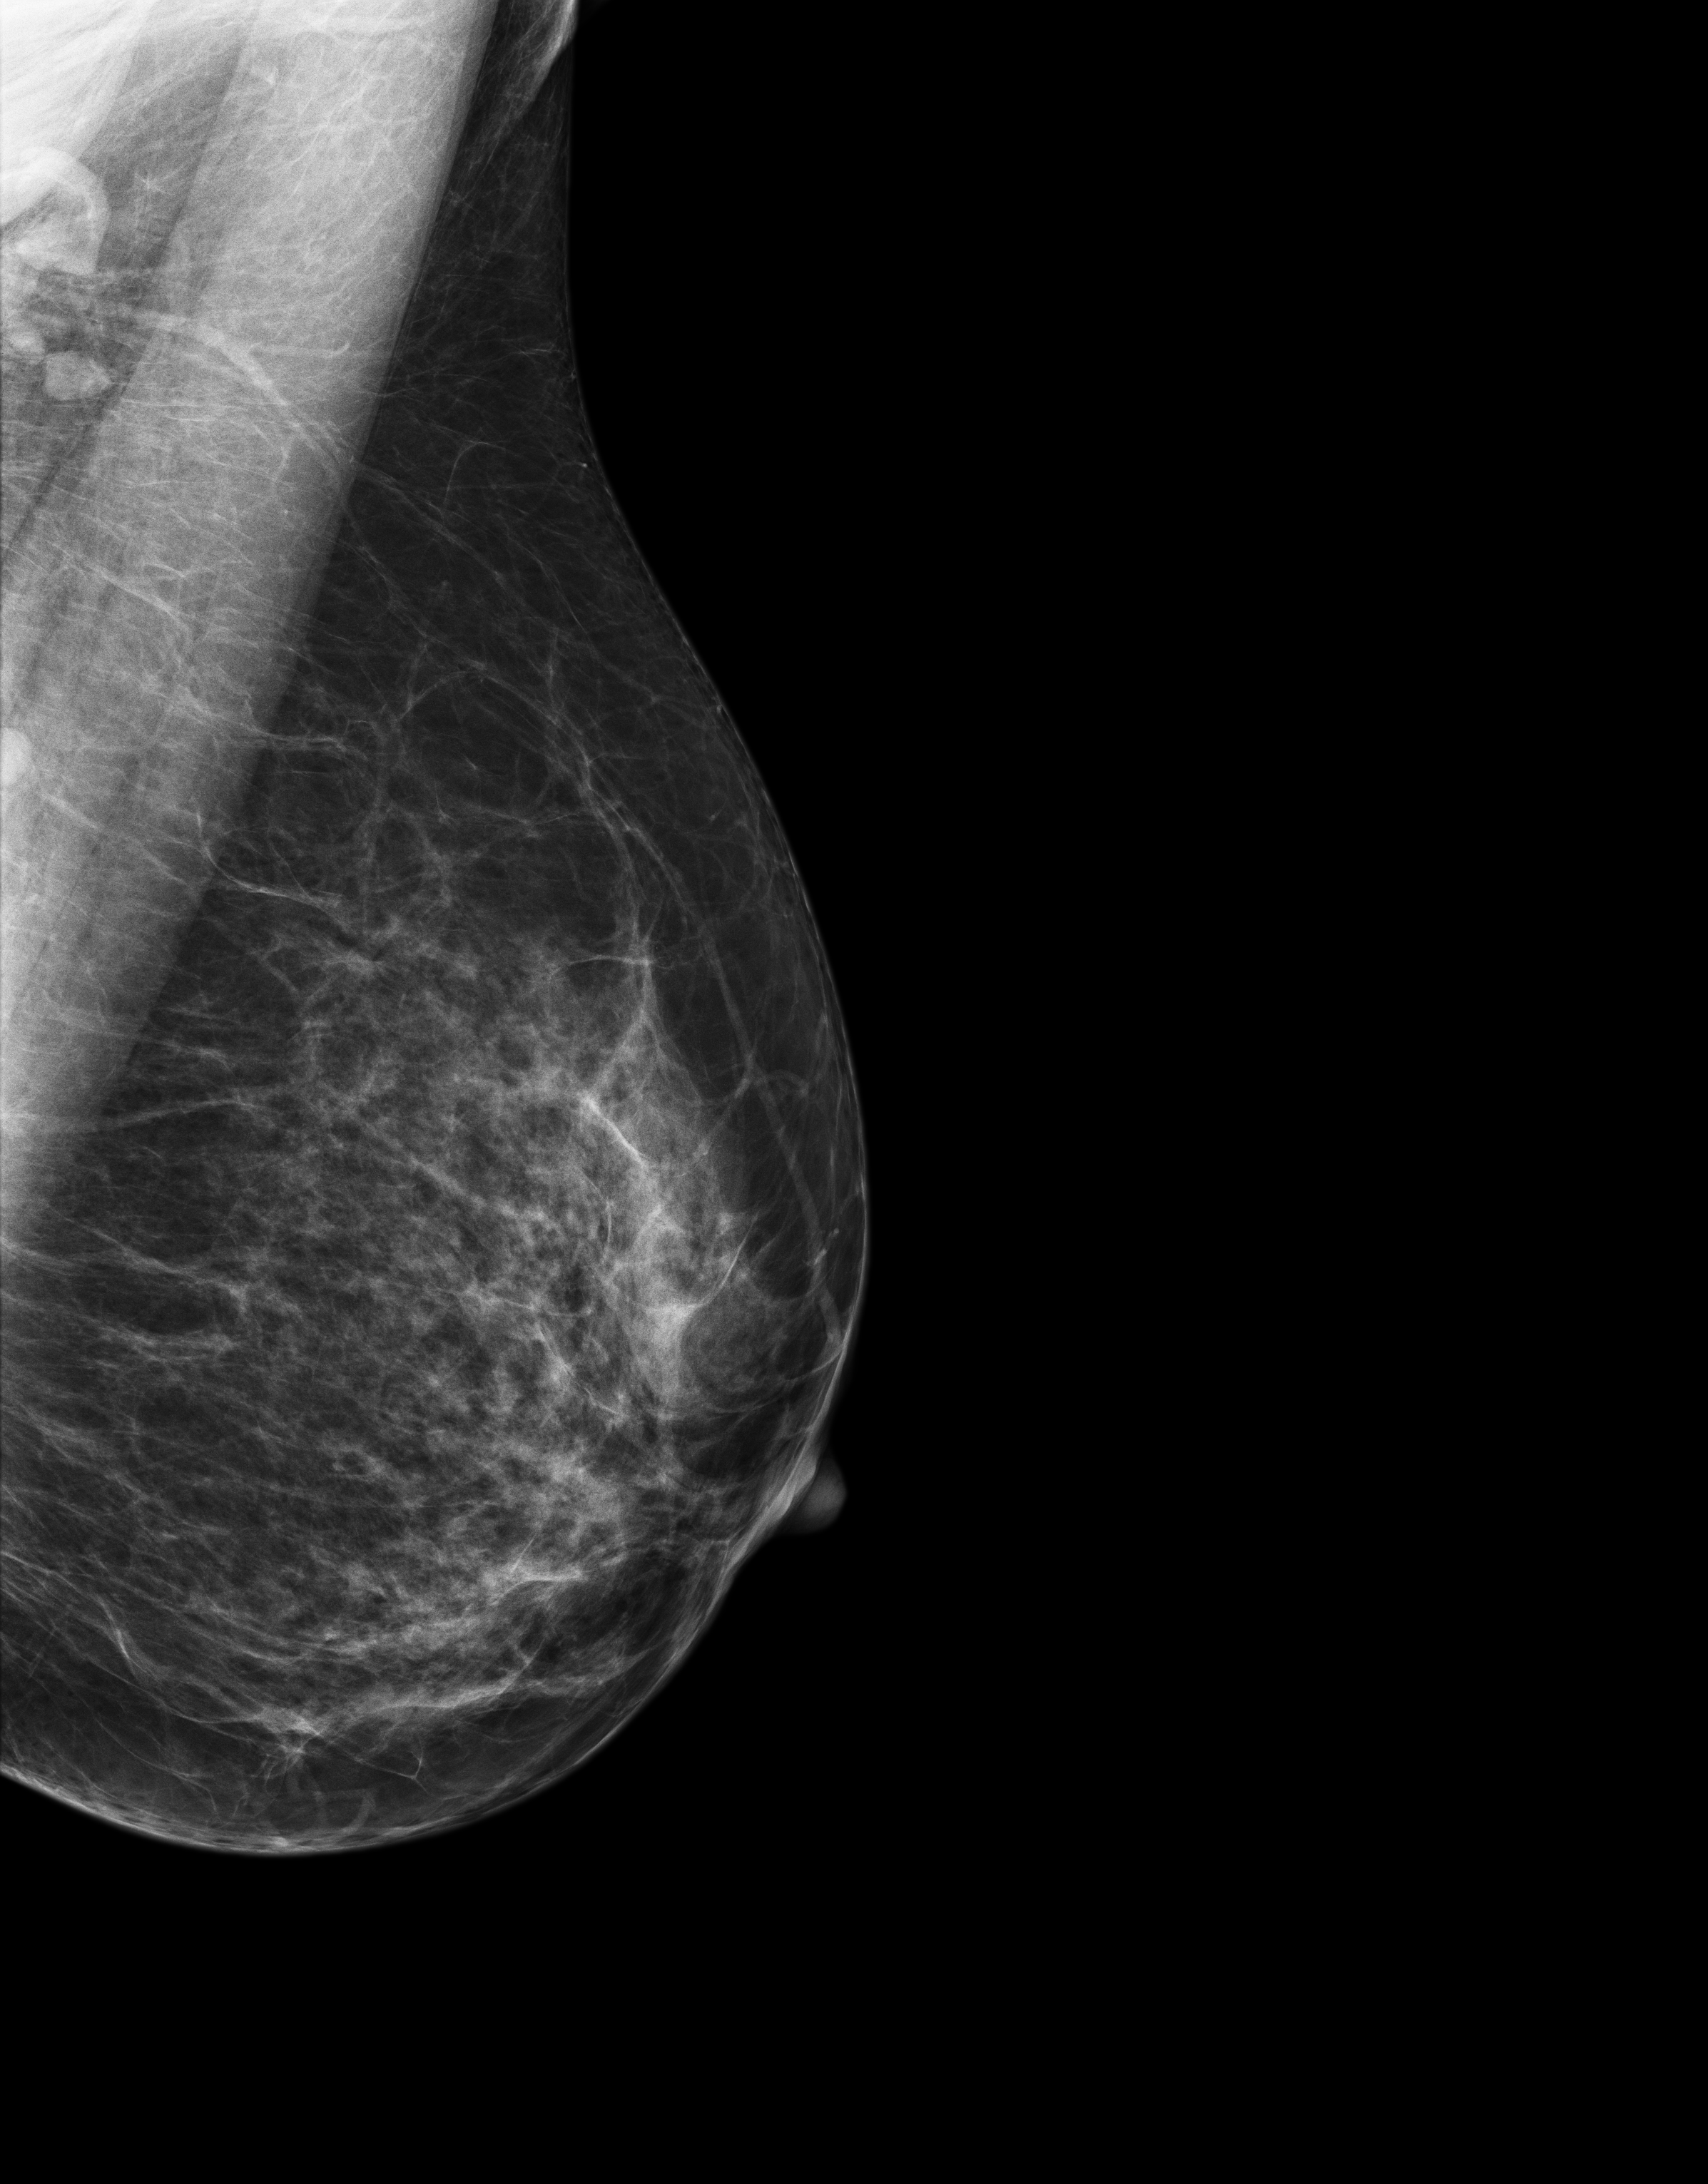
Annual screening mammography examination. Patient aged 54 years (female).
Image type: full-field digital mammogram. Breast: left. Projection: MLO view.